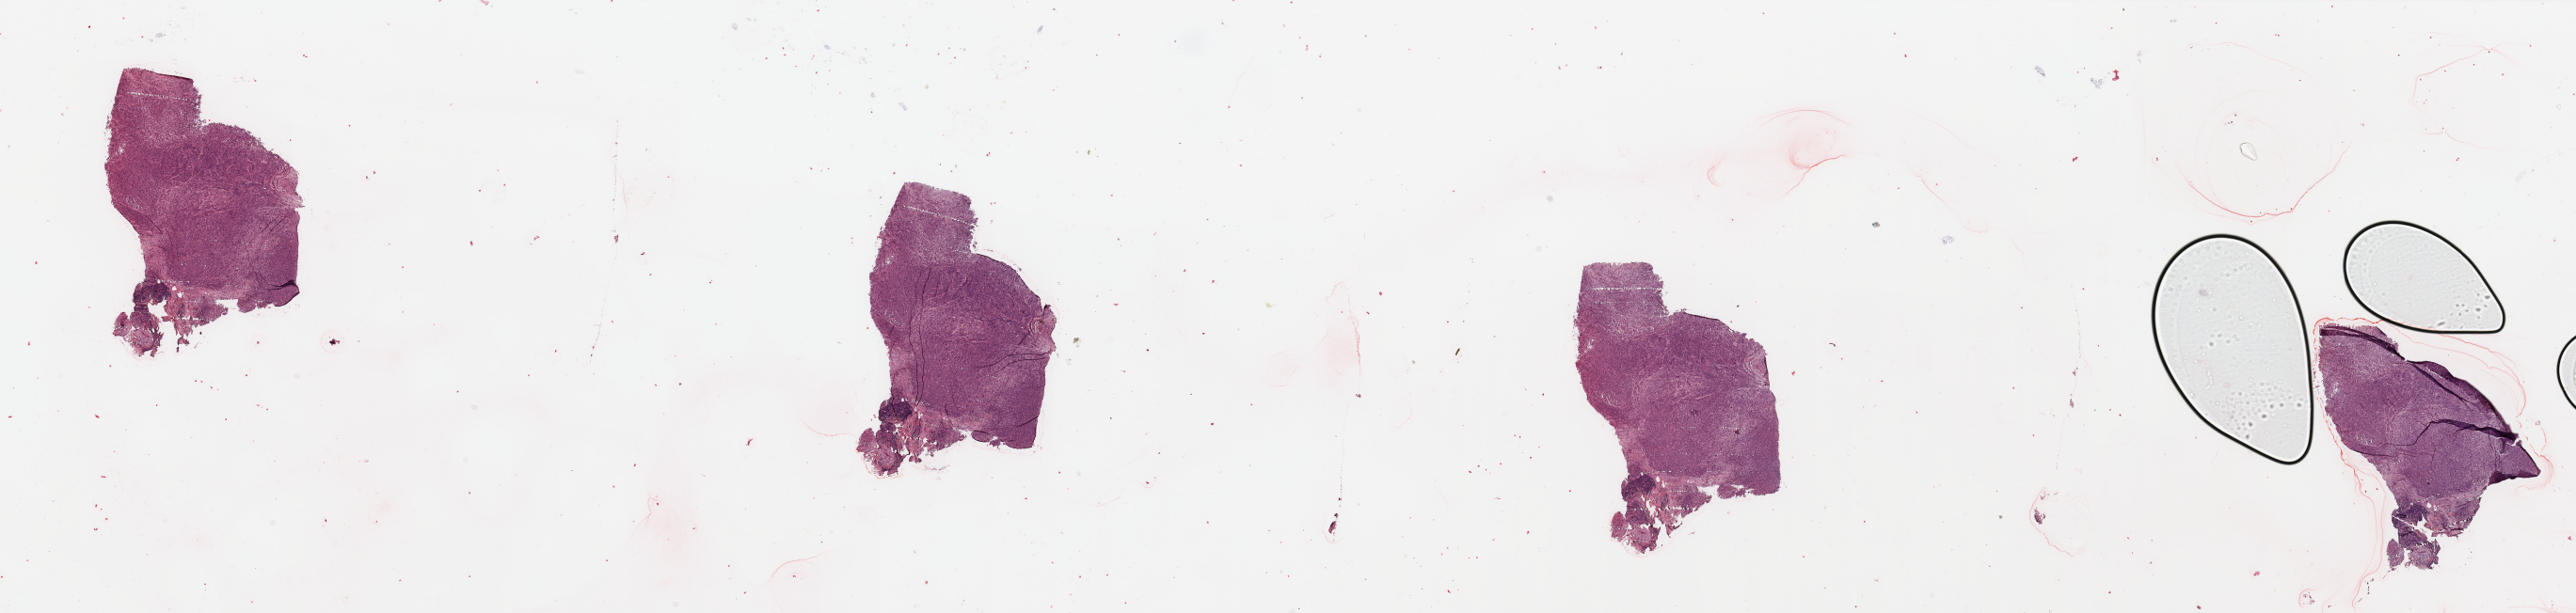
Whole-slide histology image, H&E, low-resolution overview of the scanned area, about 43.3 x 10.3 mm (acquisition: 20x scan), tumour tissue sample, sampled site: lymph node. Male, 84 y/o. Composition of this section per pathologist review: tumour nuclei 90%, necrosis 0%.
This section: metastatic tumour tissue. Patient diagnosis: Malignant melanoma, NOS.